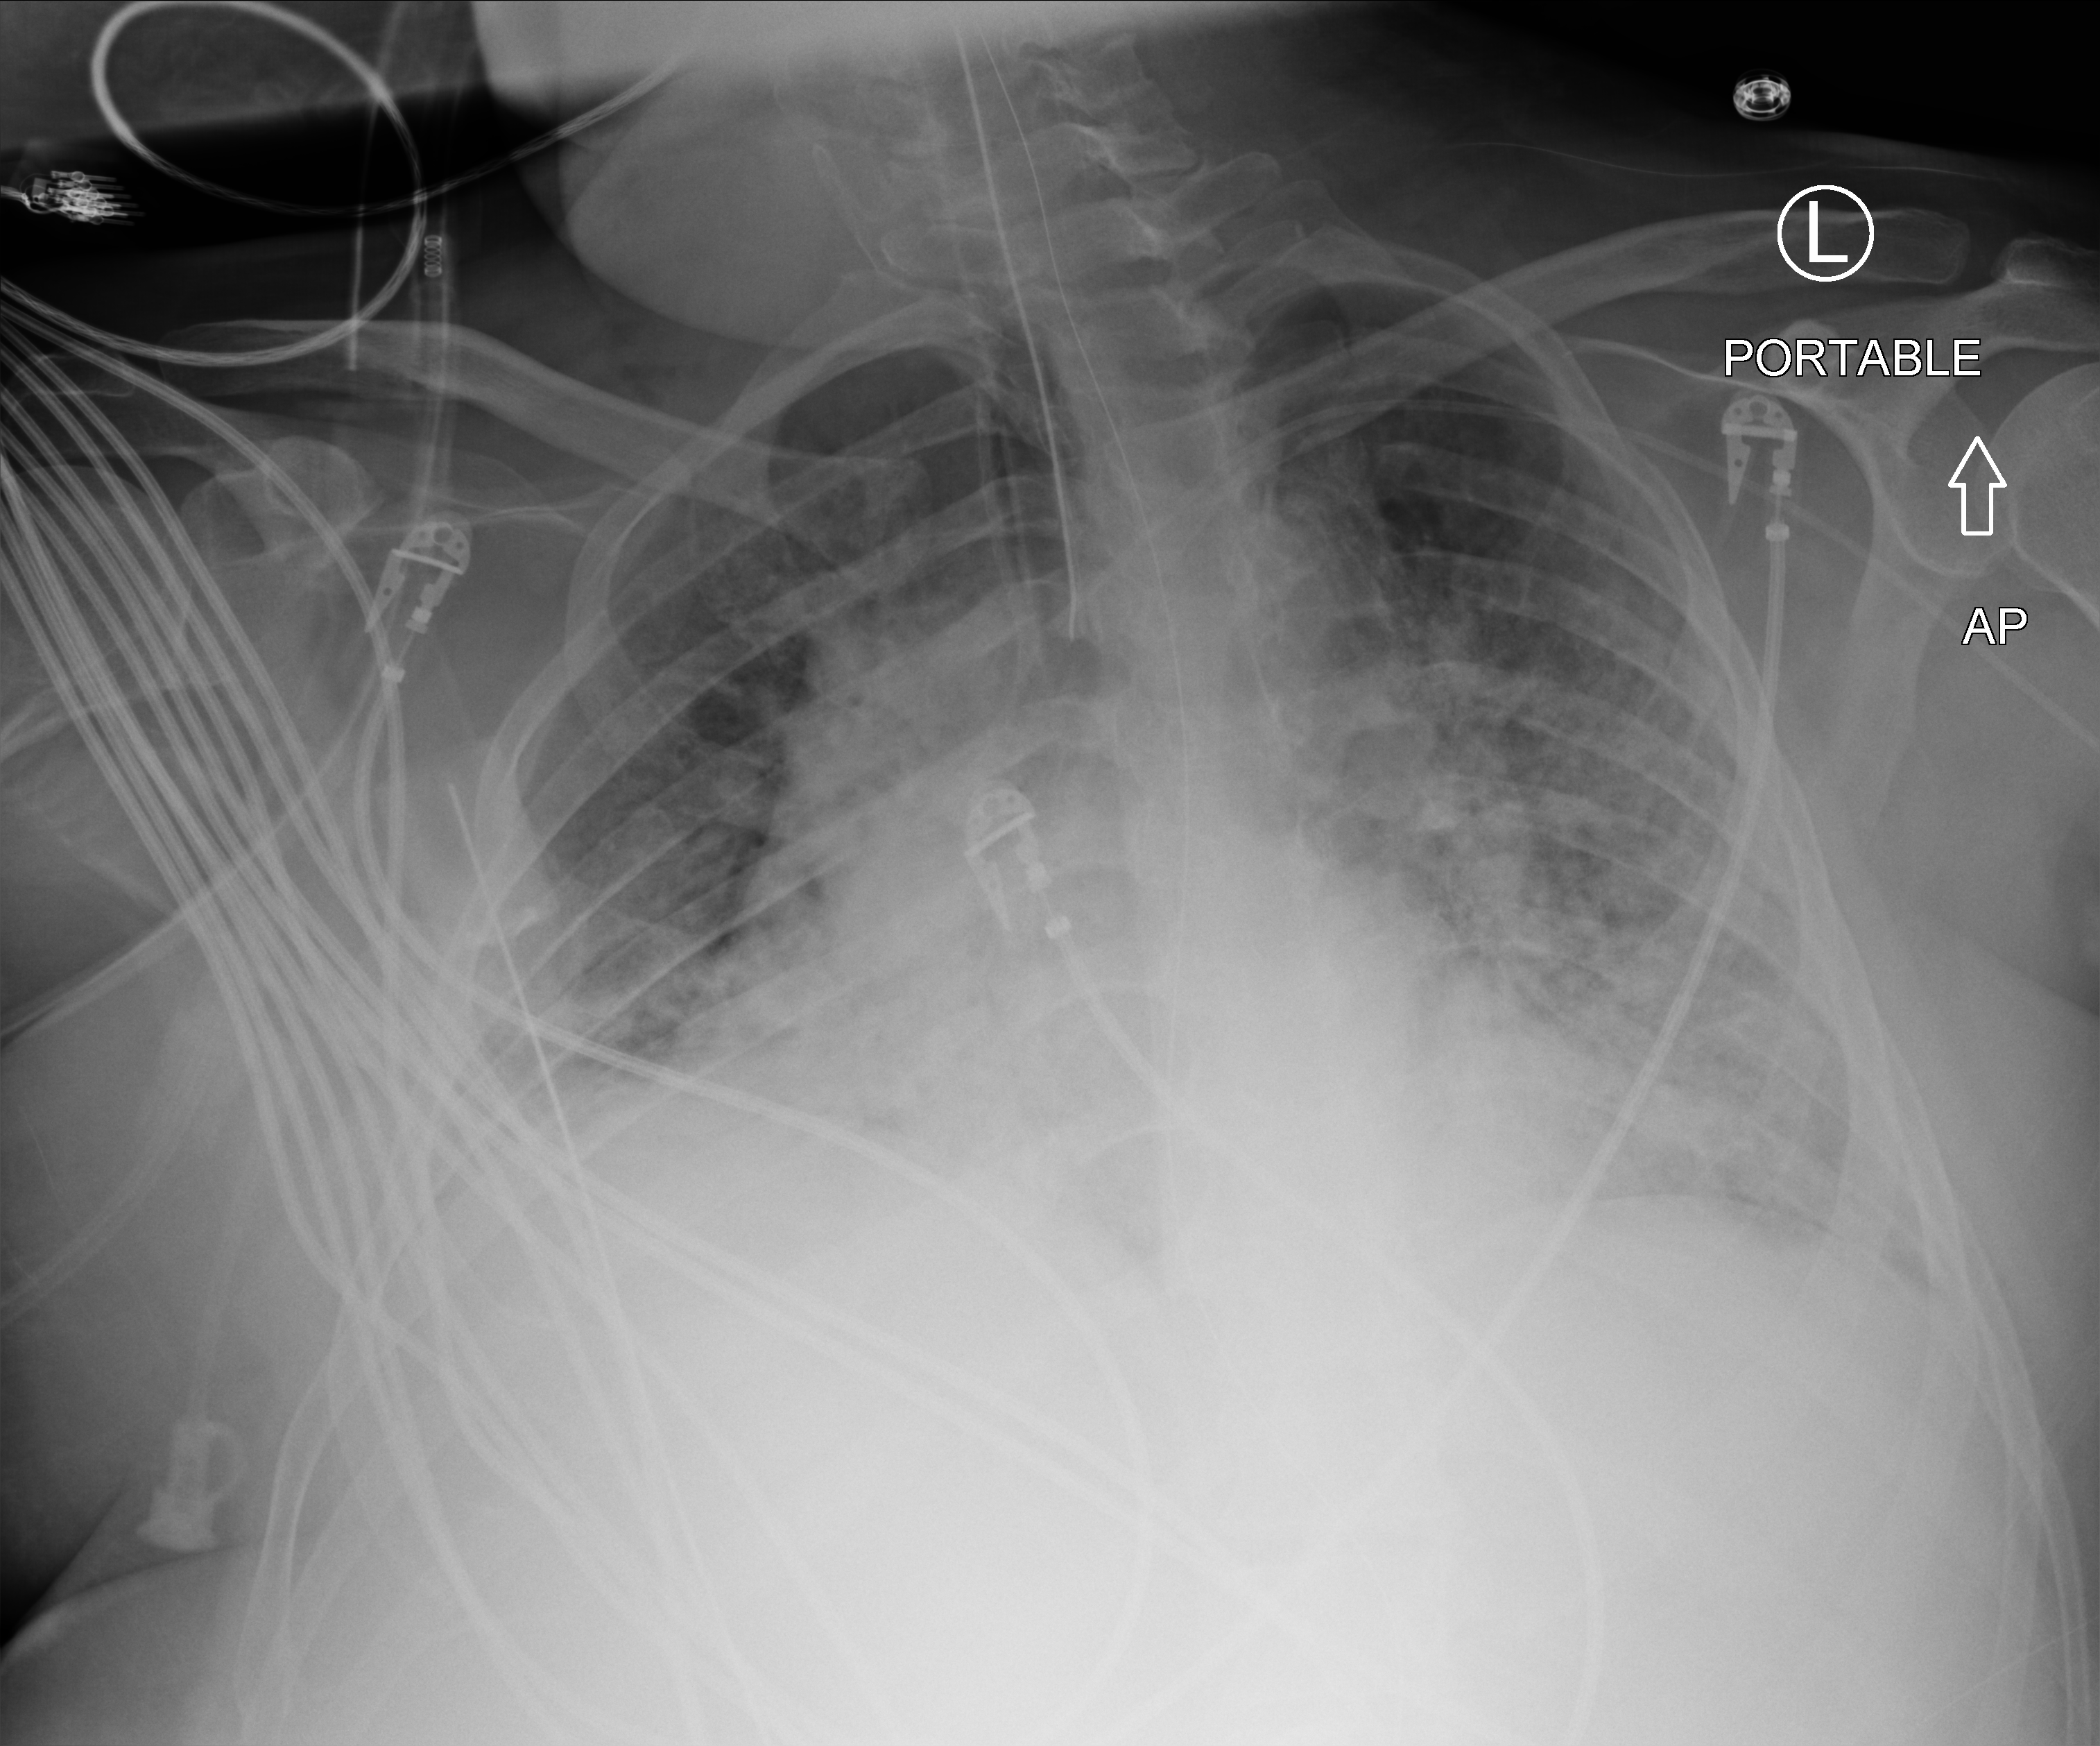
Bedside chest radiograph (computed radiography), anteroposterior (AP) projection. Patient hospitalised with COVID-19; male, aged 18–59 years.
From the hospital-stay record, not from the radiograph (when in the stay this image was taken is not recorded): COPD (admission record): no; diabetes (admission record): no; mechanically ventilated during this hospital stay: yes.